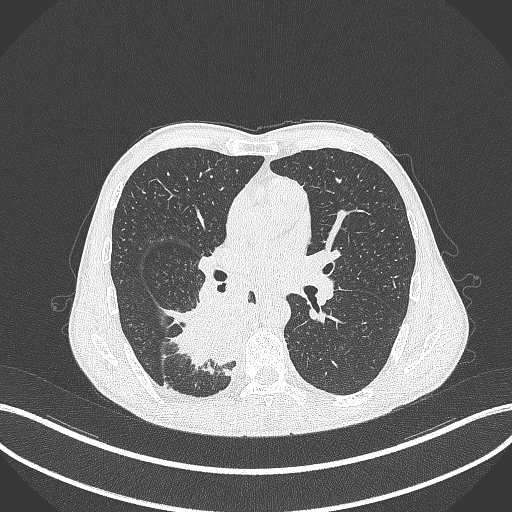
Chest CT, one axial slice; 120 kVp; lung window (W 1500 / L -600 HU); 1 mm slice thickness; 512 × 512 image matrix, field of view 400 × 400 mm. Patient: male, 58 years. Case-level facts recorded for this patient, not image findings: clinical TNM (as recorded): T3 N1 M1.
Outlined on this slice (rectangle marked by the reading radiologist):
- lung tumour (recorded histology: squamous cell carcinoma): box from (x=154, y=280) to (x=251, y=374) px